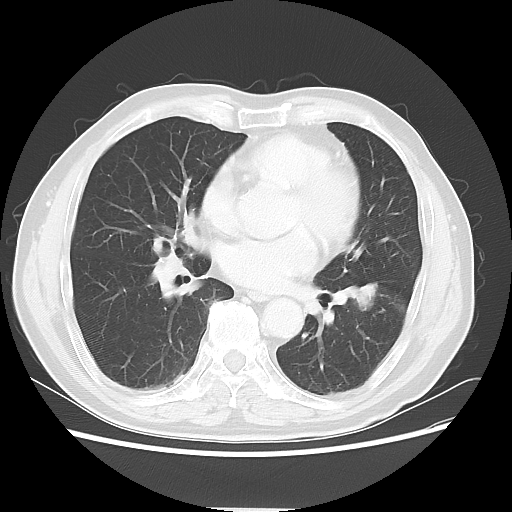
Chest CT, one axial slice. Slice 27 of 64 in the series (ordered by position). Reconstruction kernel LUNG. Lung window (W 1500 / L -600 HU). 5 mm slice thickness. 512 × 512 image matrix, field of view 366 × 366 mm. Male patient, age 71 years. Case-level facts recorded for this patient, not image findings: clinical TNM (as recorded): T1c N1 M0; histopathological grade: G2-3.
Annotated regions visible in this slice (bounding box drawn by a radiologist):
- lung tumour (recorded histology: adenocarcinoma): bounding box [x1, y1, x2, y2] px = [343, 268, 384, 321]